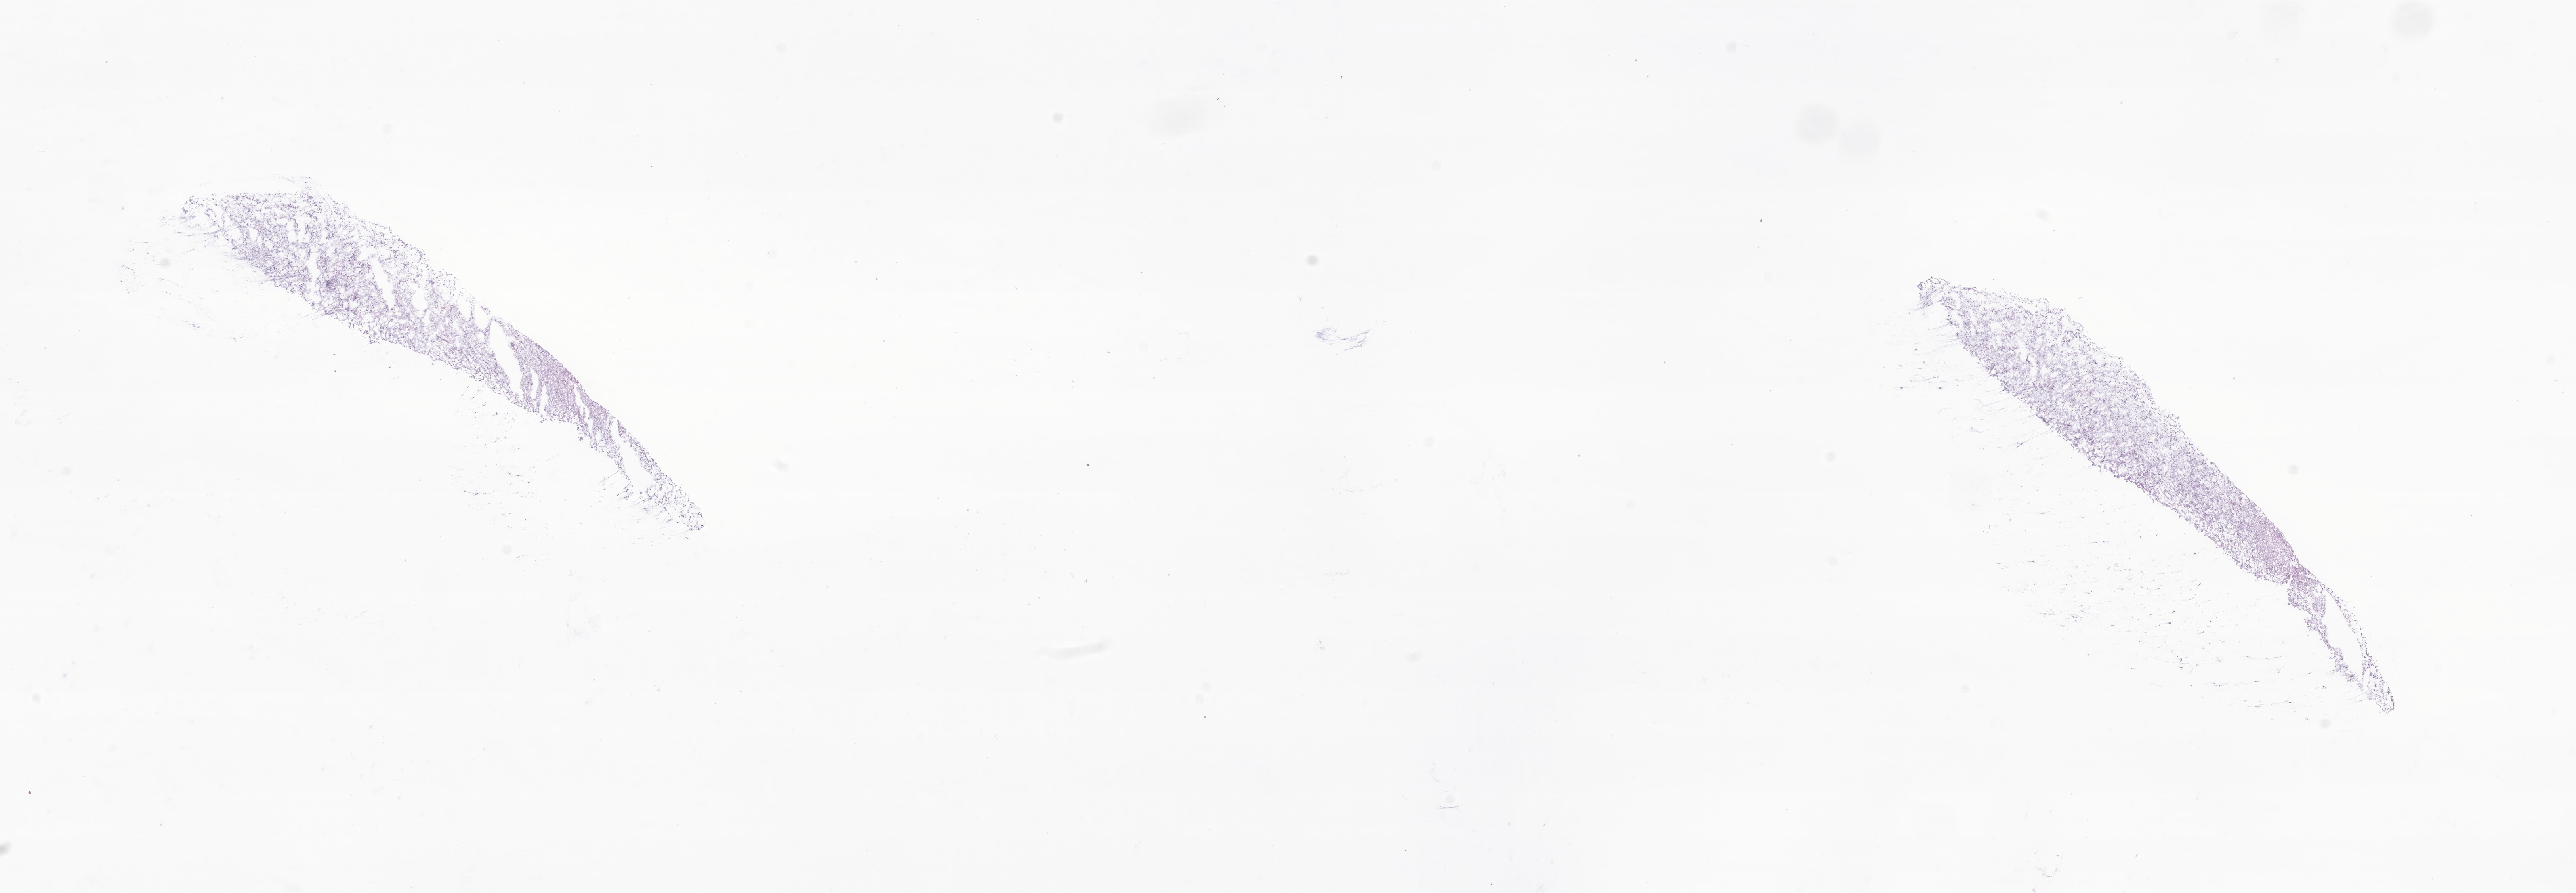
Hematoxylin and eosin (H&E) whole-slide image of tumor tissue from the frontal lobe — a low-resolution overview of the entire scanned area, about 27.4 x 9.5 mm; frozen section. Patient: male, age 71 months (5 years 11 months).
• diagnosis: Dysembryoplastic neuroepithelial tumor